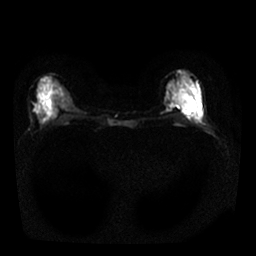
Breast MRI, one axial slice; position 10 of 25 along the scan axis; diffusion-weighted series; image 2 of 4 stored at this slice position (different b-values; order by instance number); 1.5 T; 4 mm slice thickness; 256 × 256 image matrix. Female patient.
Structures marked on this image (expert manual segmentation):
- tumour on diffusion-weighted imaging: box from (x=179, y=92) to (x=196, y=112) px